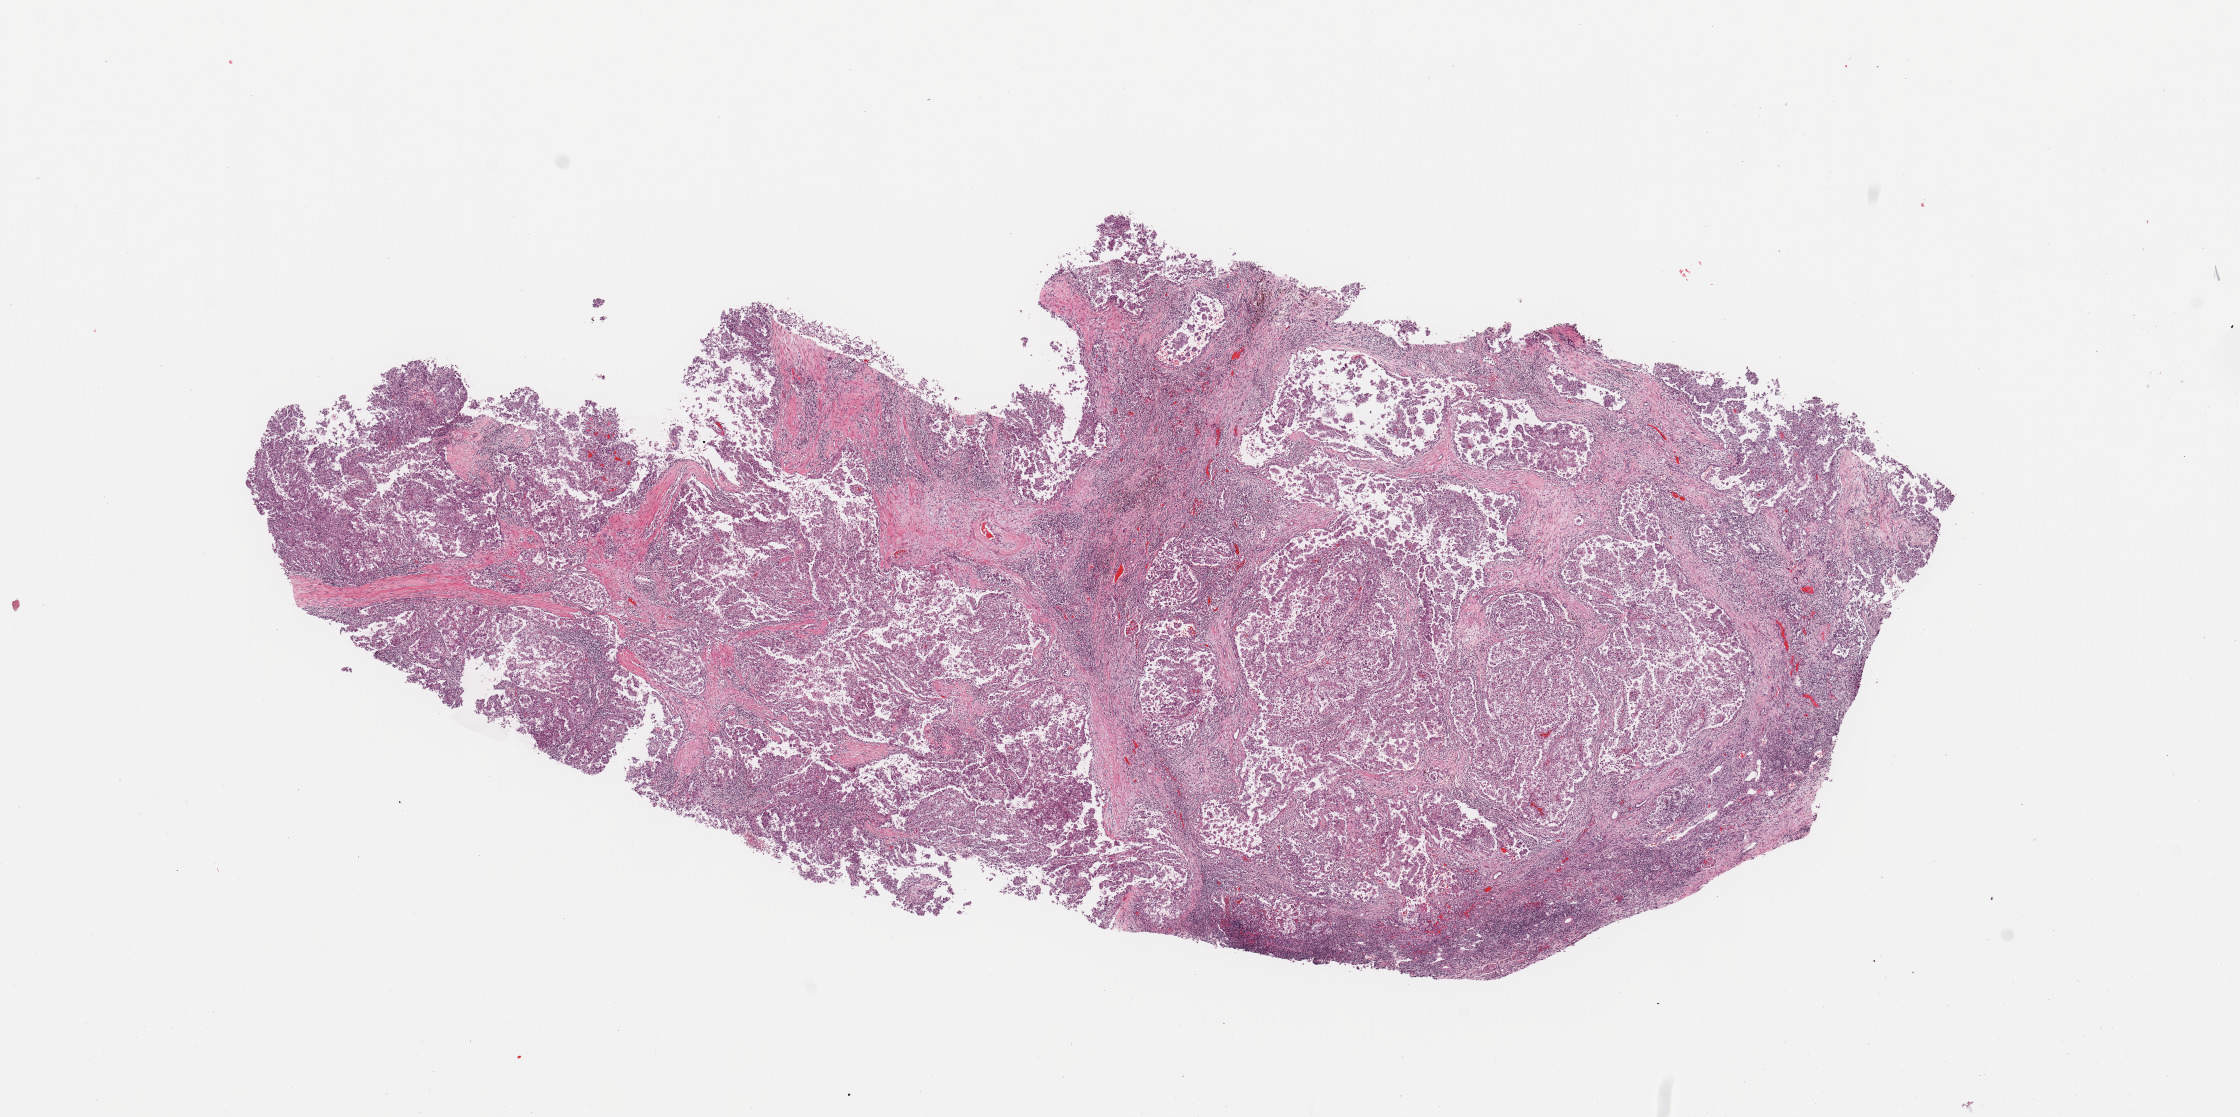
Digitized Hematoxylin and eosin (H&E) stained tissue section (whole slide) — low-resolution overview of the scanned area, about 17.7 x 8.8 mm (acquisition: 20x scan), tumour tissue sample, sampled site: kidney. 50-year-old male patient. Histologic grade: G2 (moderately differentiated). Pathologist review of this section (percent, as recorded): tumour nuclei 85%, necrosis 2%.
• AJCC pathologic stage: III
• diagnosis: Renal cell carcinoma, NOS